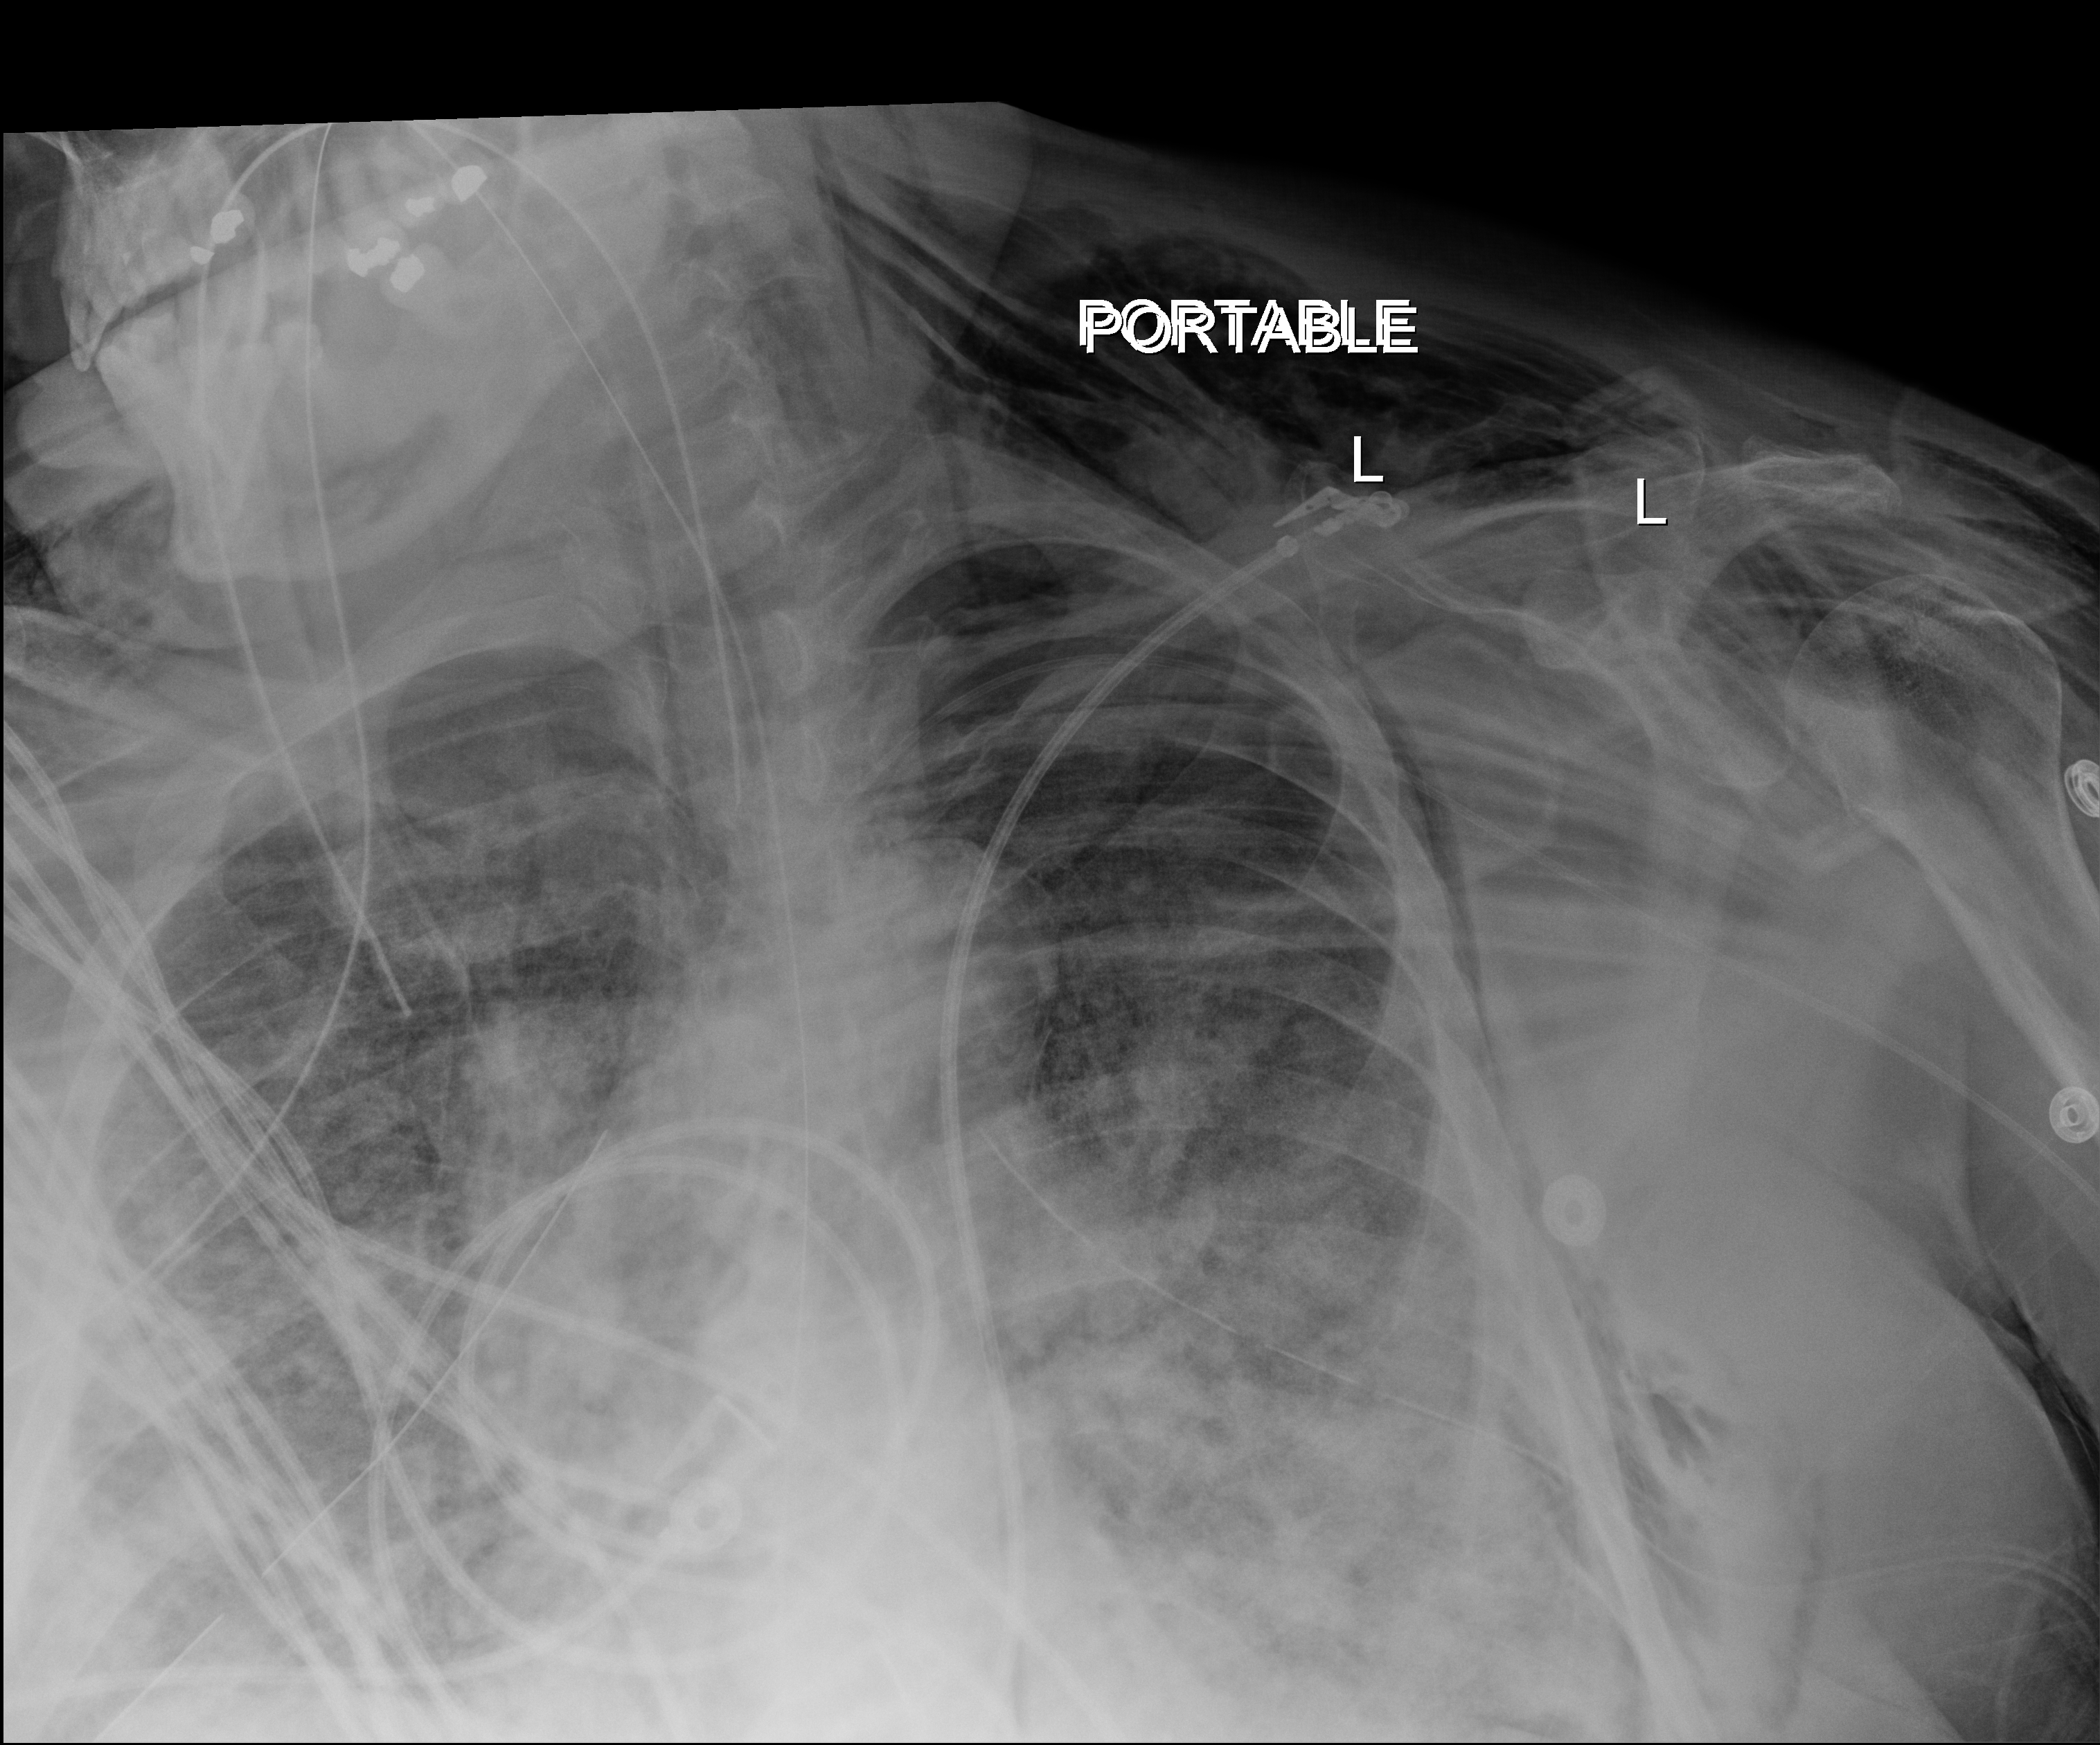
Chest X-ray. Patient hospitalised with COVID-19, aged 18–59 years.
Admission-level facts for this patient (not findings on this image; timing relative to this image not recorded): mechanically ventilated during this hospital stay: yes.